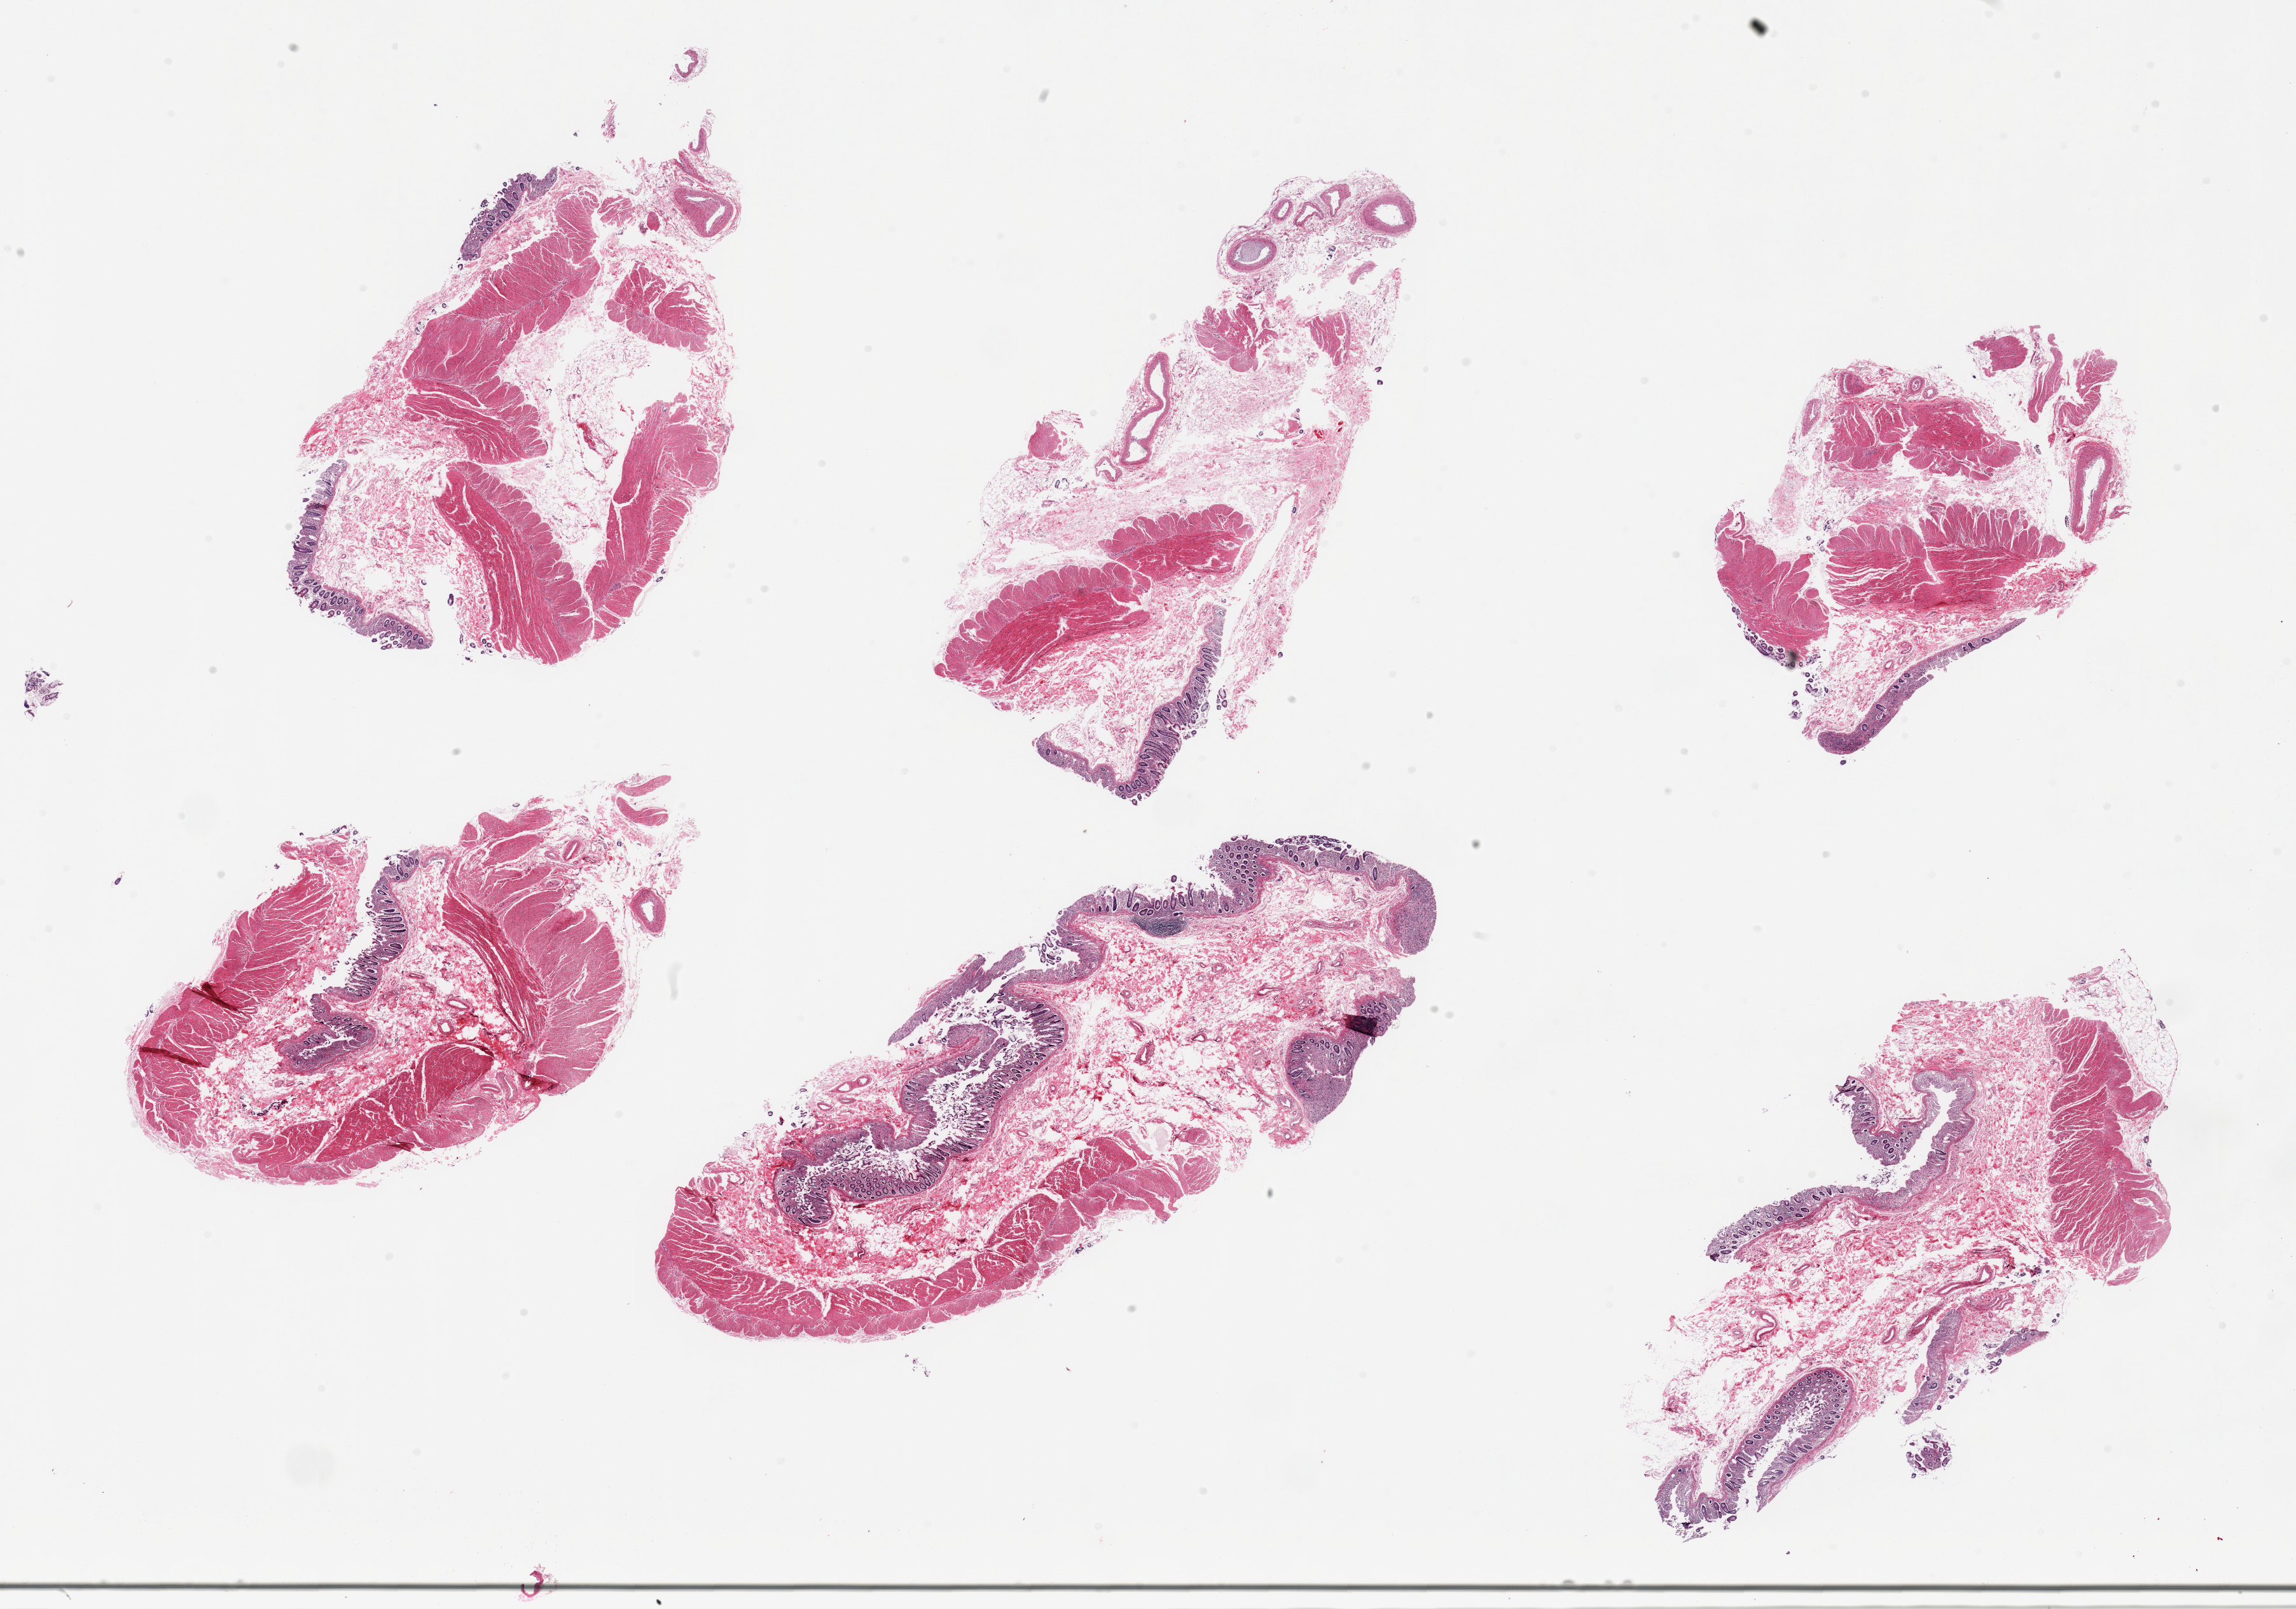
Whole-slide image, haematoxylin and eosin stain, a low-resolution overview of the entire scanned area, about 28.5 x 20.0 mm (from a 20x scan). PAXgene-fixed, paraffin-embedded tissue. Target tissue: transverse colon. Donor tissue sample. Donor: female.
Review note (as recorded): 6 pieces; all are full thickness.